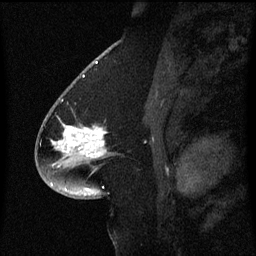
Breast MRI (dynamic contrast-enhanced), one sagittal slice; slice 32 of 60 in the series (ordered by position); dynamic contrast-enhanced series, image 2 of 3 at this slice position (ordered by acquisition); 1.5 T; TE 4.2 ms, TR 8.4 ms; 2 mm slice thickness; 256 × 256 image matrix. Patient: female, 54 years. From the clinical record (not read from this slice): setting: breast cancer imaged before/during neoadjuvant chemotherapy; receptor status: HR-positive, HER2-negative.
Annotated regions visible in this slice (semi-automatic segmentation, software-assisted and operator-edited):
- analysis volume of interest (the breast-tissue region the enhancement analysis was run in; not a lesion): box from (x=46, y=100) to (x=115, y=169) px
- tumour enhancement mask (voxels above the 70 % enhancement threshold inside the analysis volume of interest): (x=53, y=126)–(x=105, y=151)